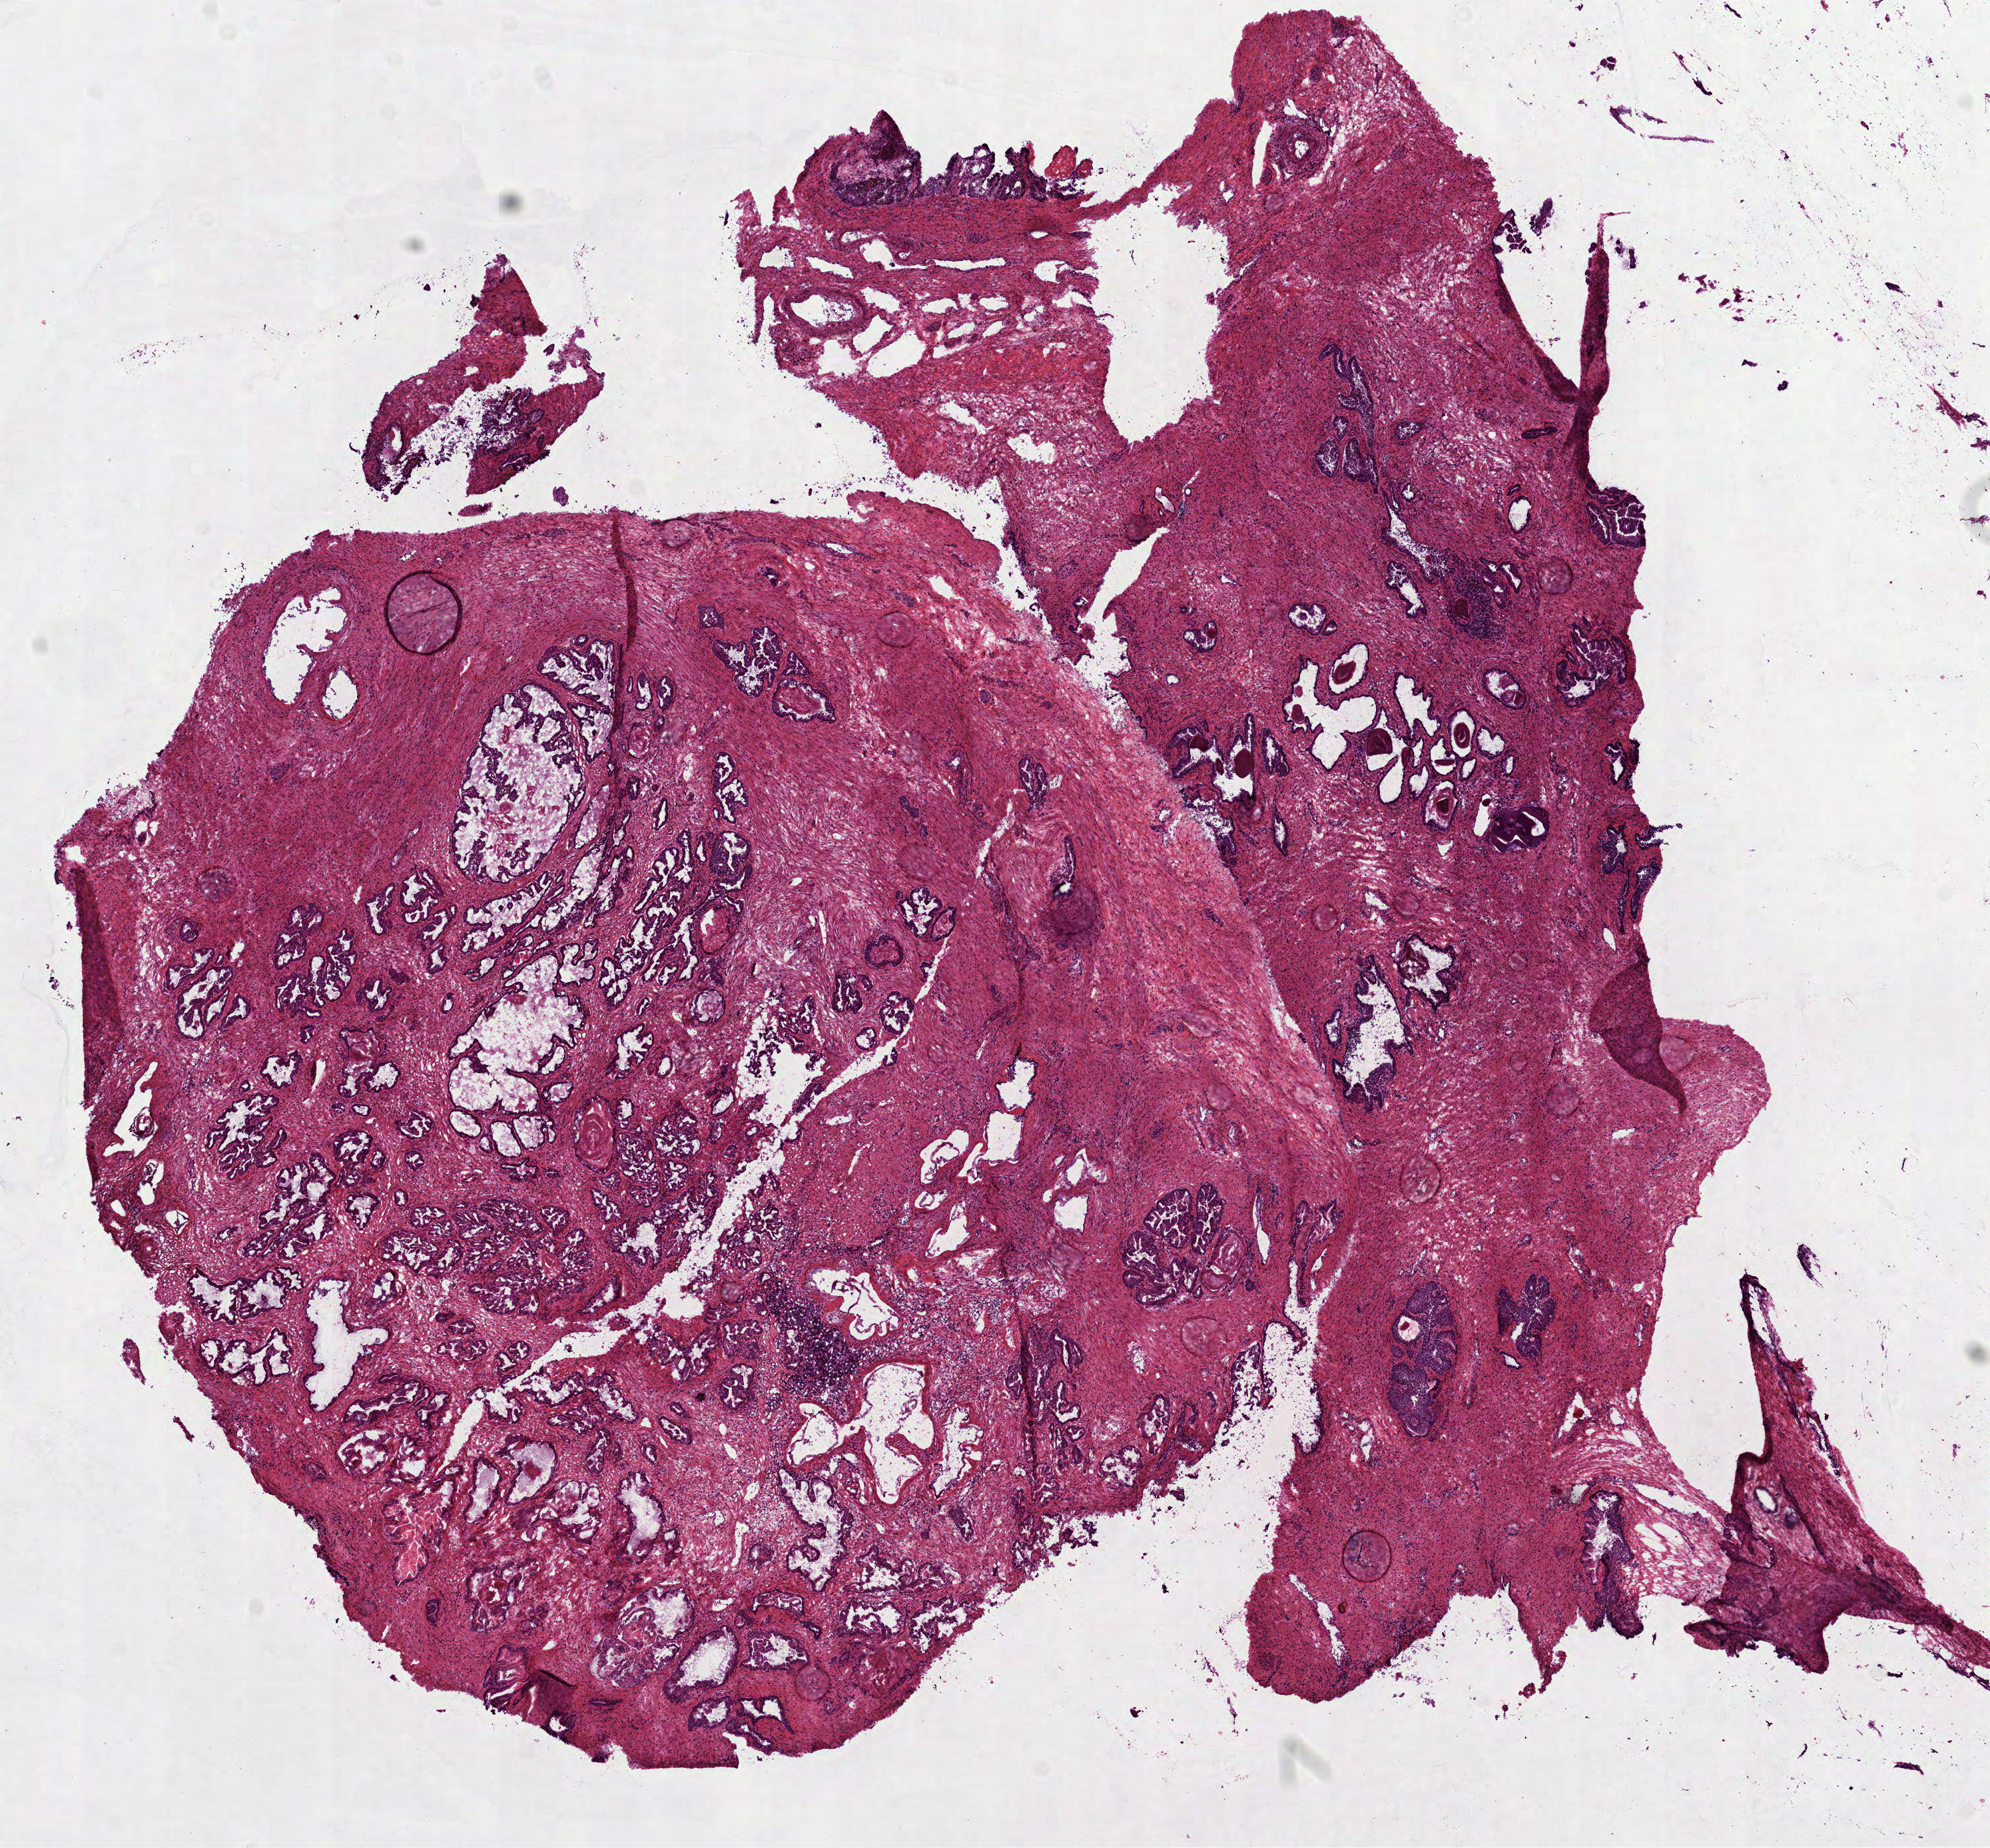
Whole-slide histology image, H&E-stained — shown as a low-resolution overview of the whole scanned area (about 12.0 x 11.2 mm, acquisition: 40x scan). Frozen section from the top of the tissue portion. Solid tissue normal (non-tumour tissue) sample from the prostate. Male, age 61 years at initial diagnosis.
* this section: solid tissue normal sample (biorepository sample class)
* patient diagnosis: Acinar cell carcinoma